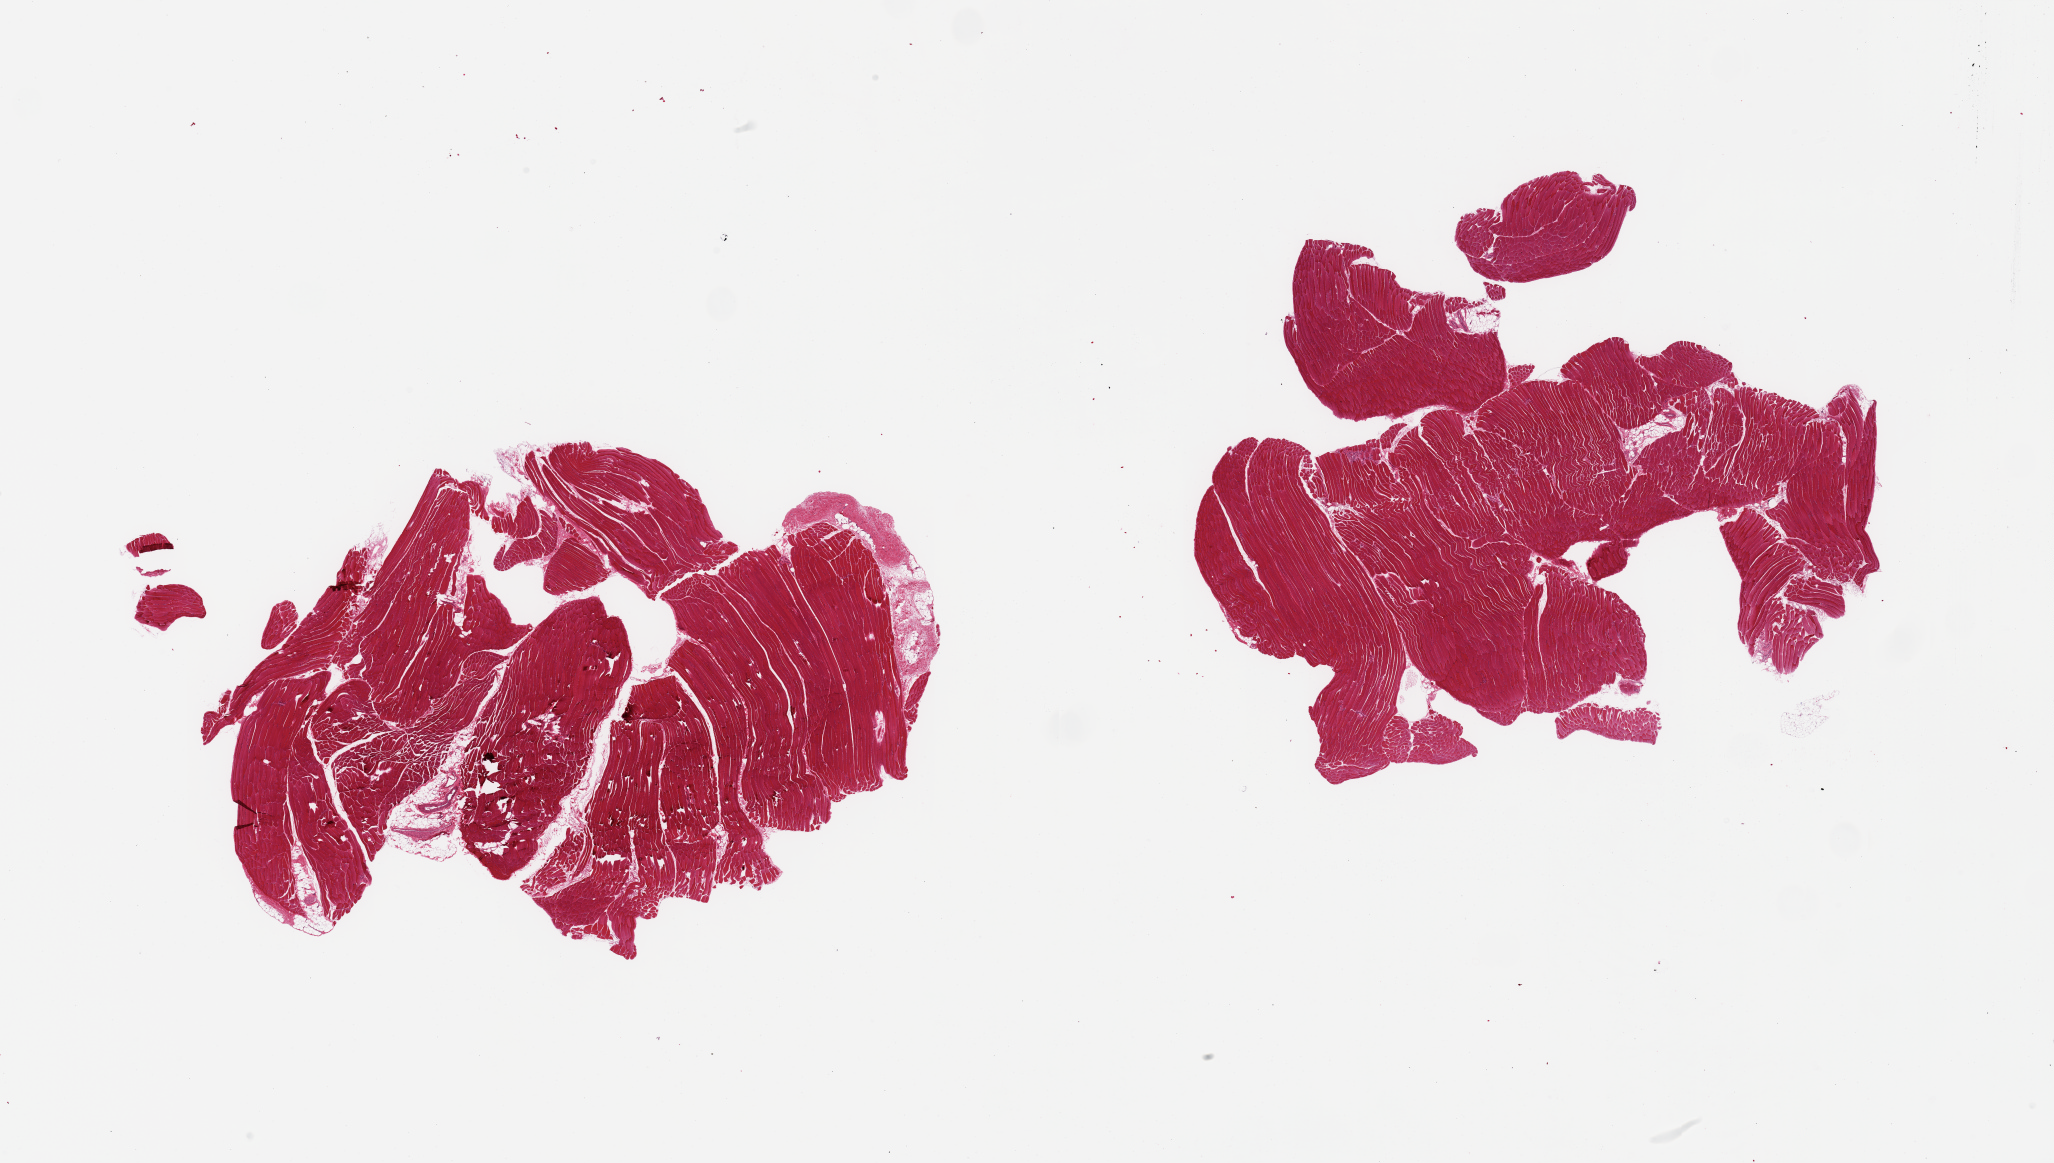
Whole-slide image, haematoxylin and eosin stain, low-resolution overview of the scanned area, about 32.5 x 18.4 mm. PAXgene-fixed, paraffin-embedded tissue. Section of skeletal muscle (target tissue). Donor tissue sample. Male donor.
Review note (as recorded): 2 pieces, interstitial/adherent fat/vascular elements.